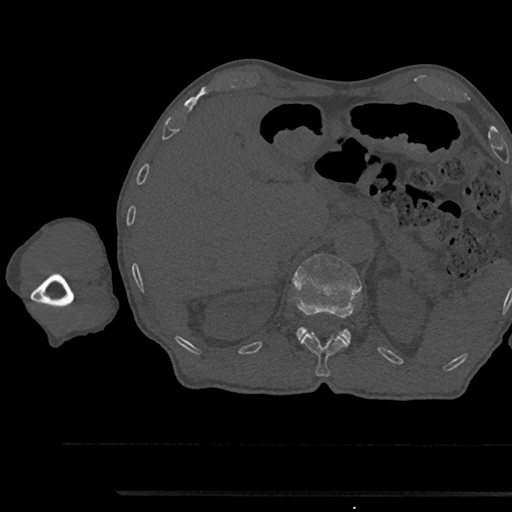
CT including the spine, one axial slice. Slice 682 of 797 in the series (ordered by position). 120 kVp. Bone window (W 1800 / L 400 HU). 0.5 mm slice thickness. 512 × 512 image matrix, field of view 367 × 367 mm. Male patient, age 79 years. From the clinical record (not read from this slice): primary cancer: prostate.
Annotated regions visible in this slice (semi-automatic segmentation, software-assisted and operator-edited):
- L1 vertebra: box from (x=292, y=254) to (x=362, y=342) px
- T12 vertebra: (x=301, y=333)–(x=349, y=377)